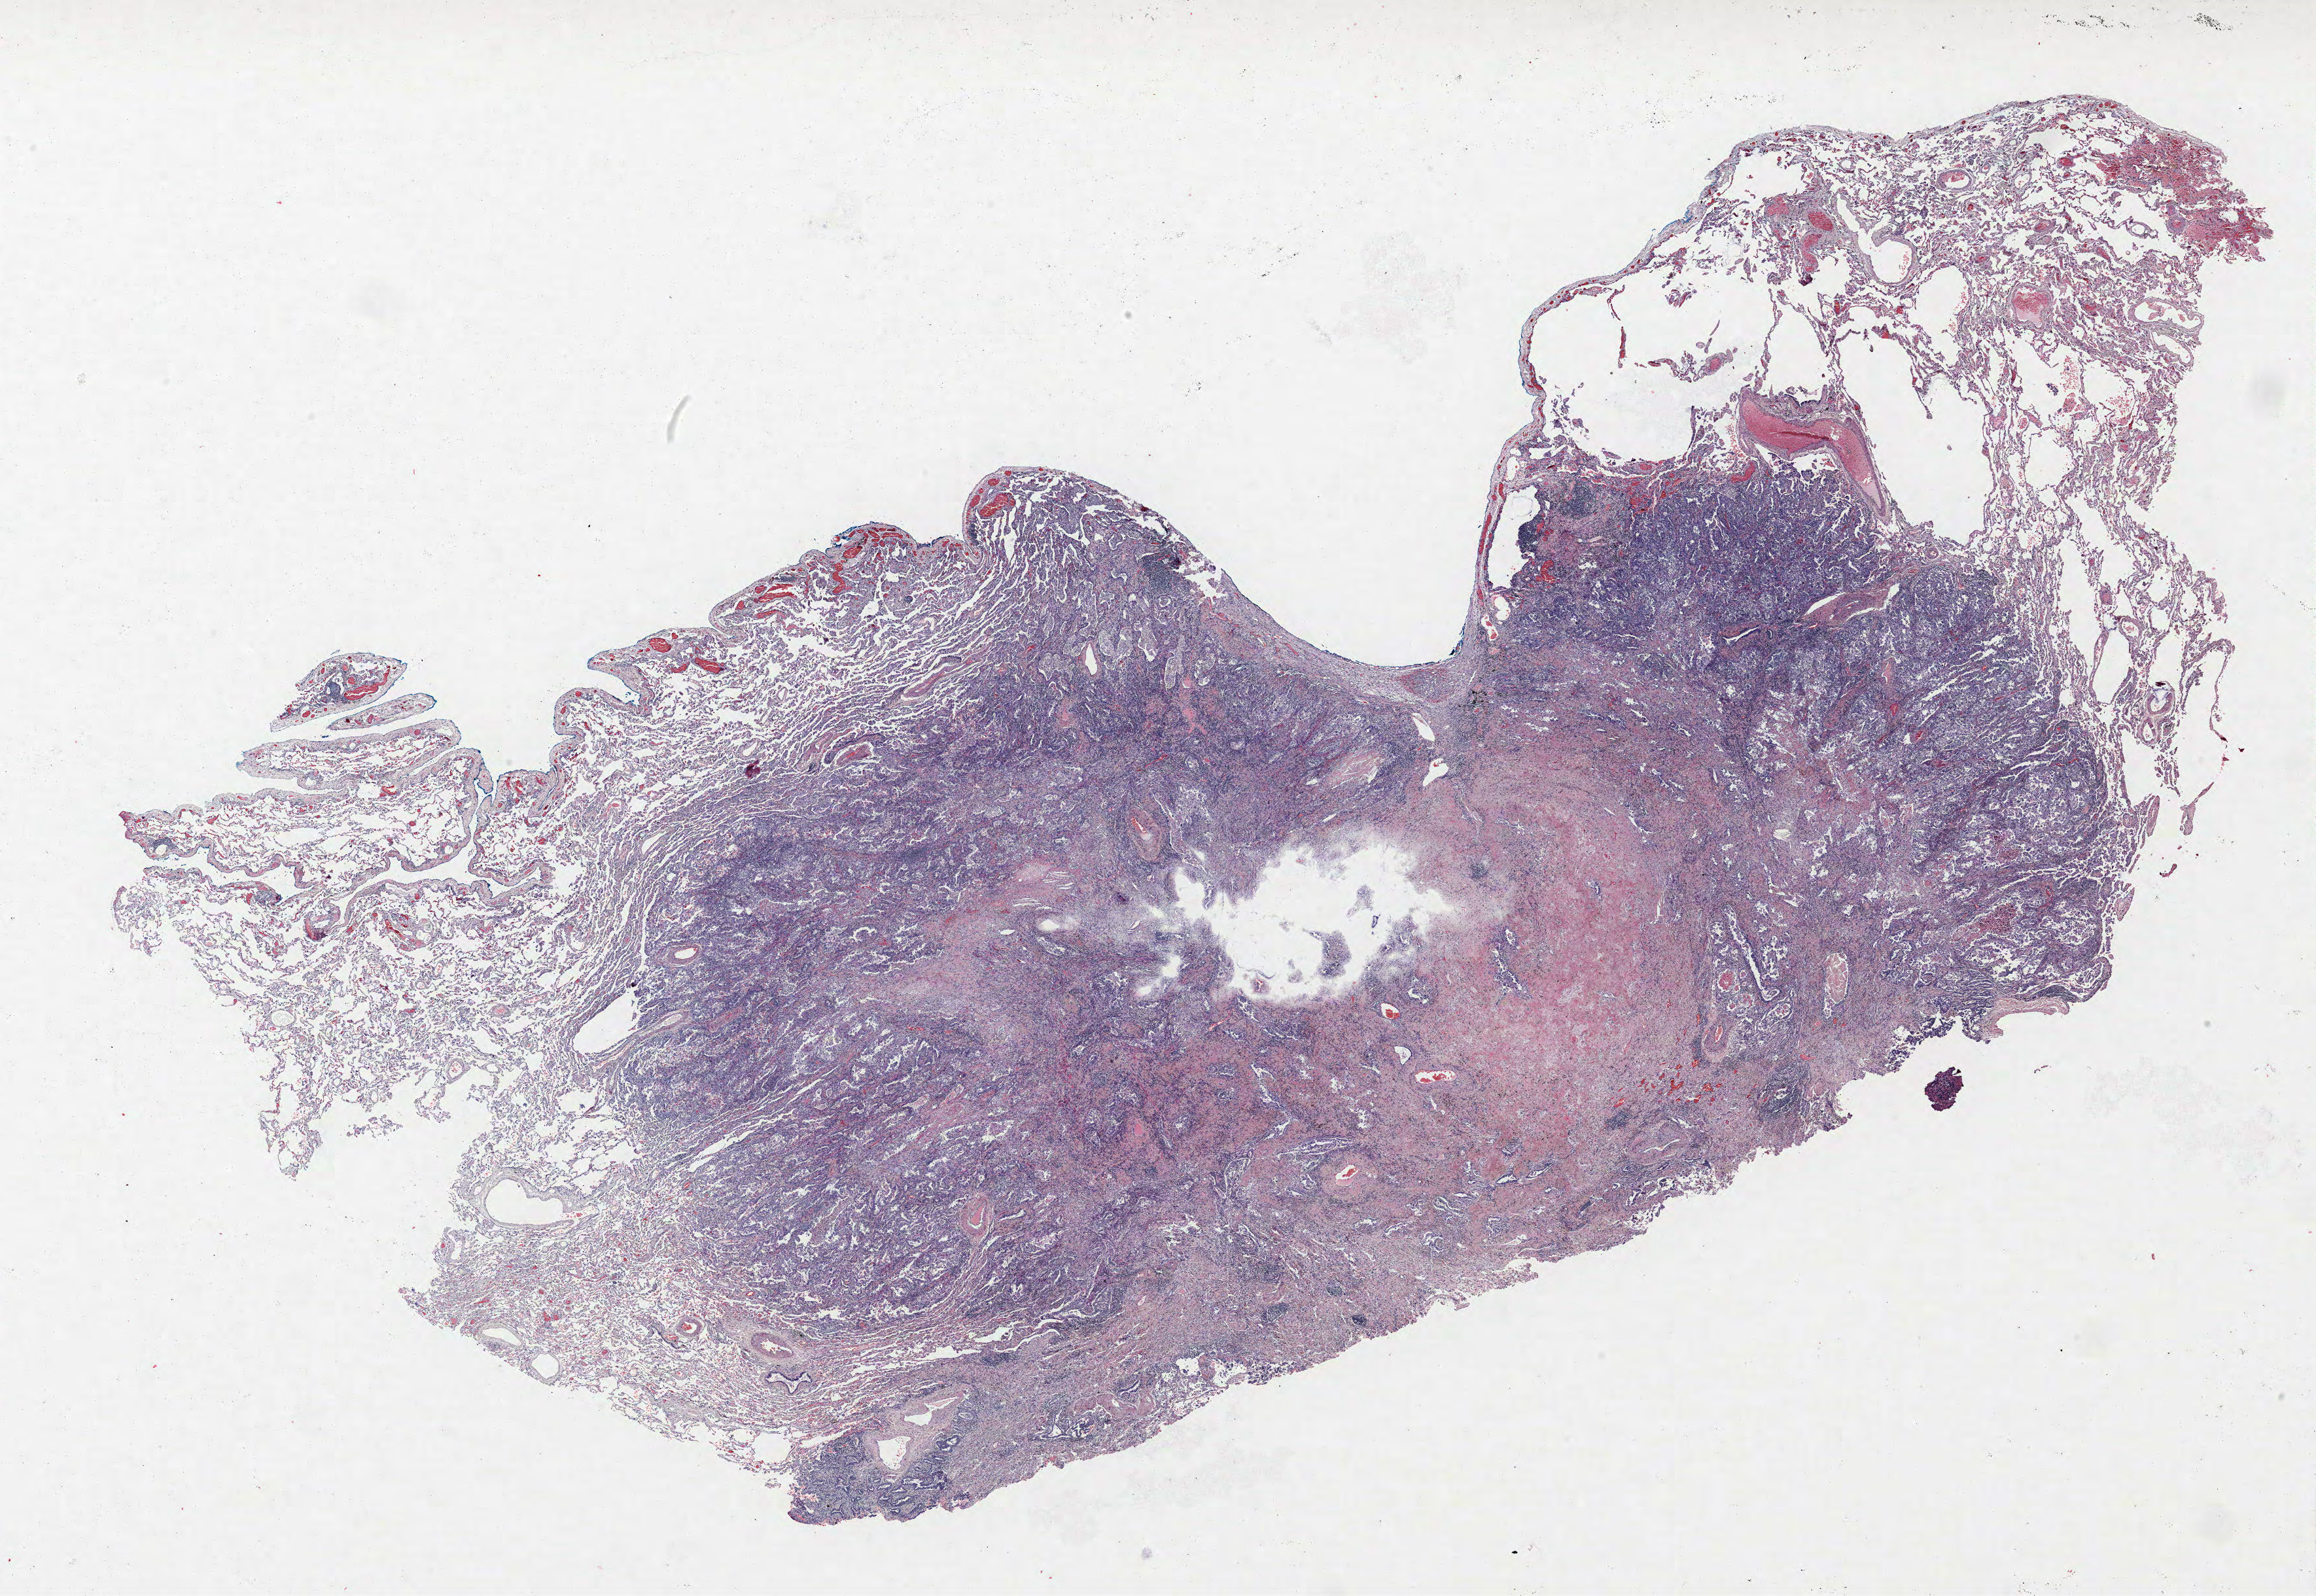
H&E whole-slide image, whole scanned area (about 28.3 x 19.5 mm, acquisition: 40x scan) shown as a low-resolution overview; FFPE section; lung. Male patient, aged 70 at enrolment. Current smoker at enrolment. Grade: poorly differentiated (G3).
Participant's lung-cancer diagnosis: Adenocarcinoma, NOS (ICD-O-3 8140/3). Primary tumour location (clinical record): right upper lobe. Stage (AJCC 6th edition): IA. Tumour size (pathology): 20 mm.